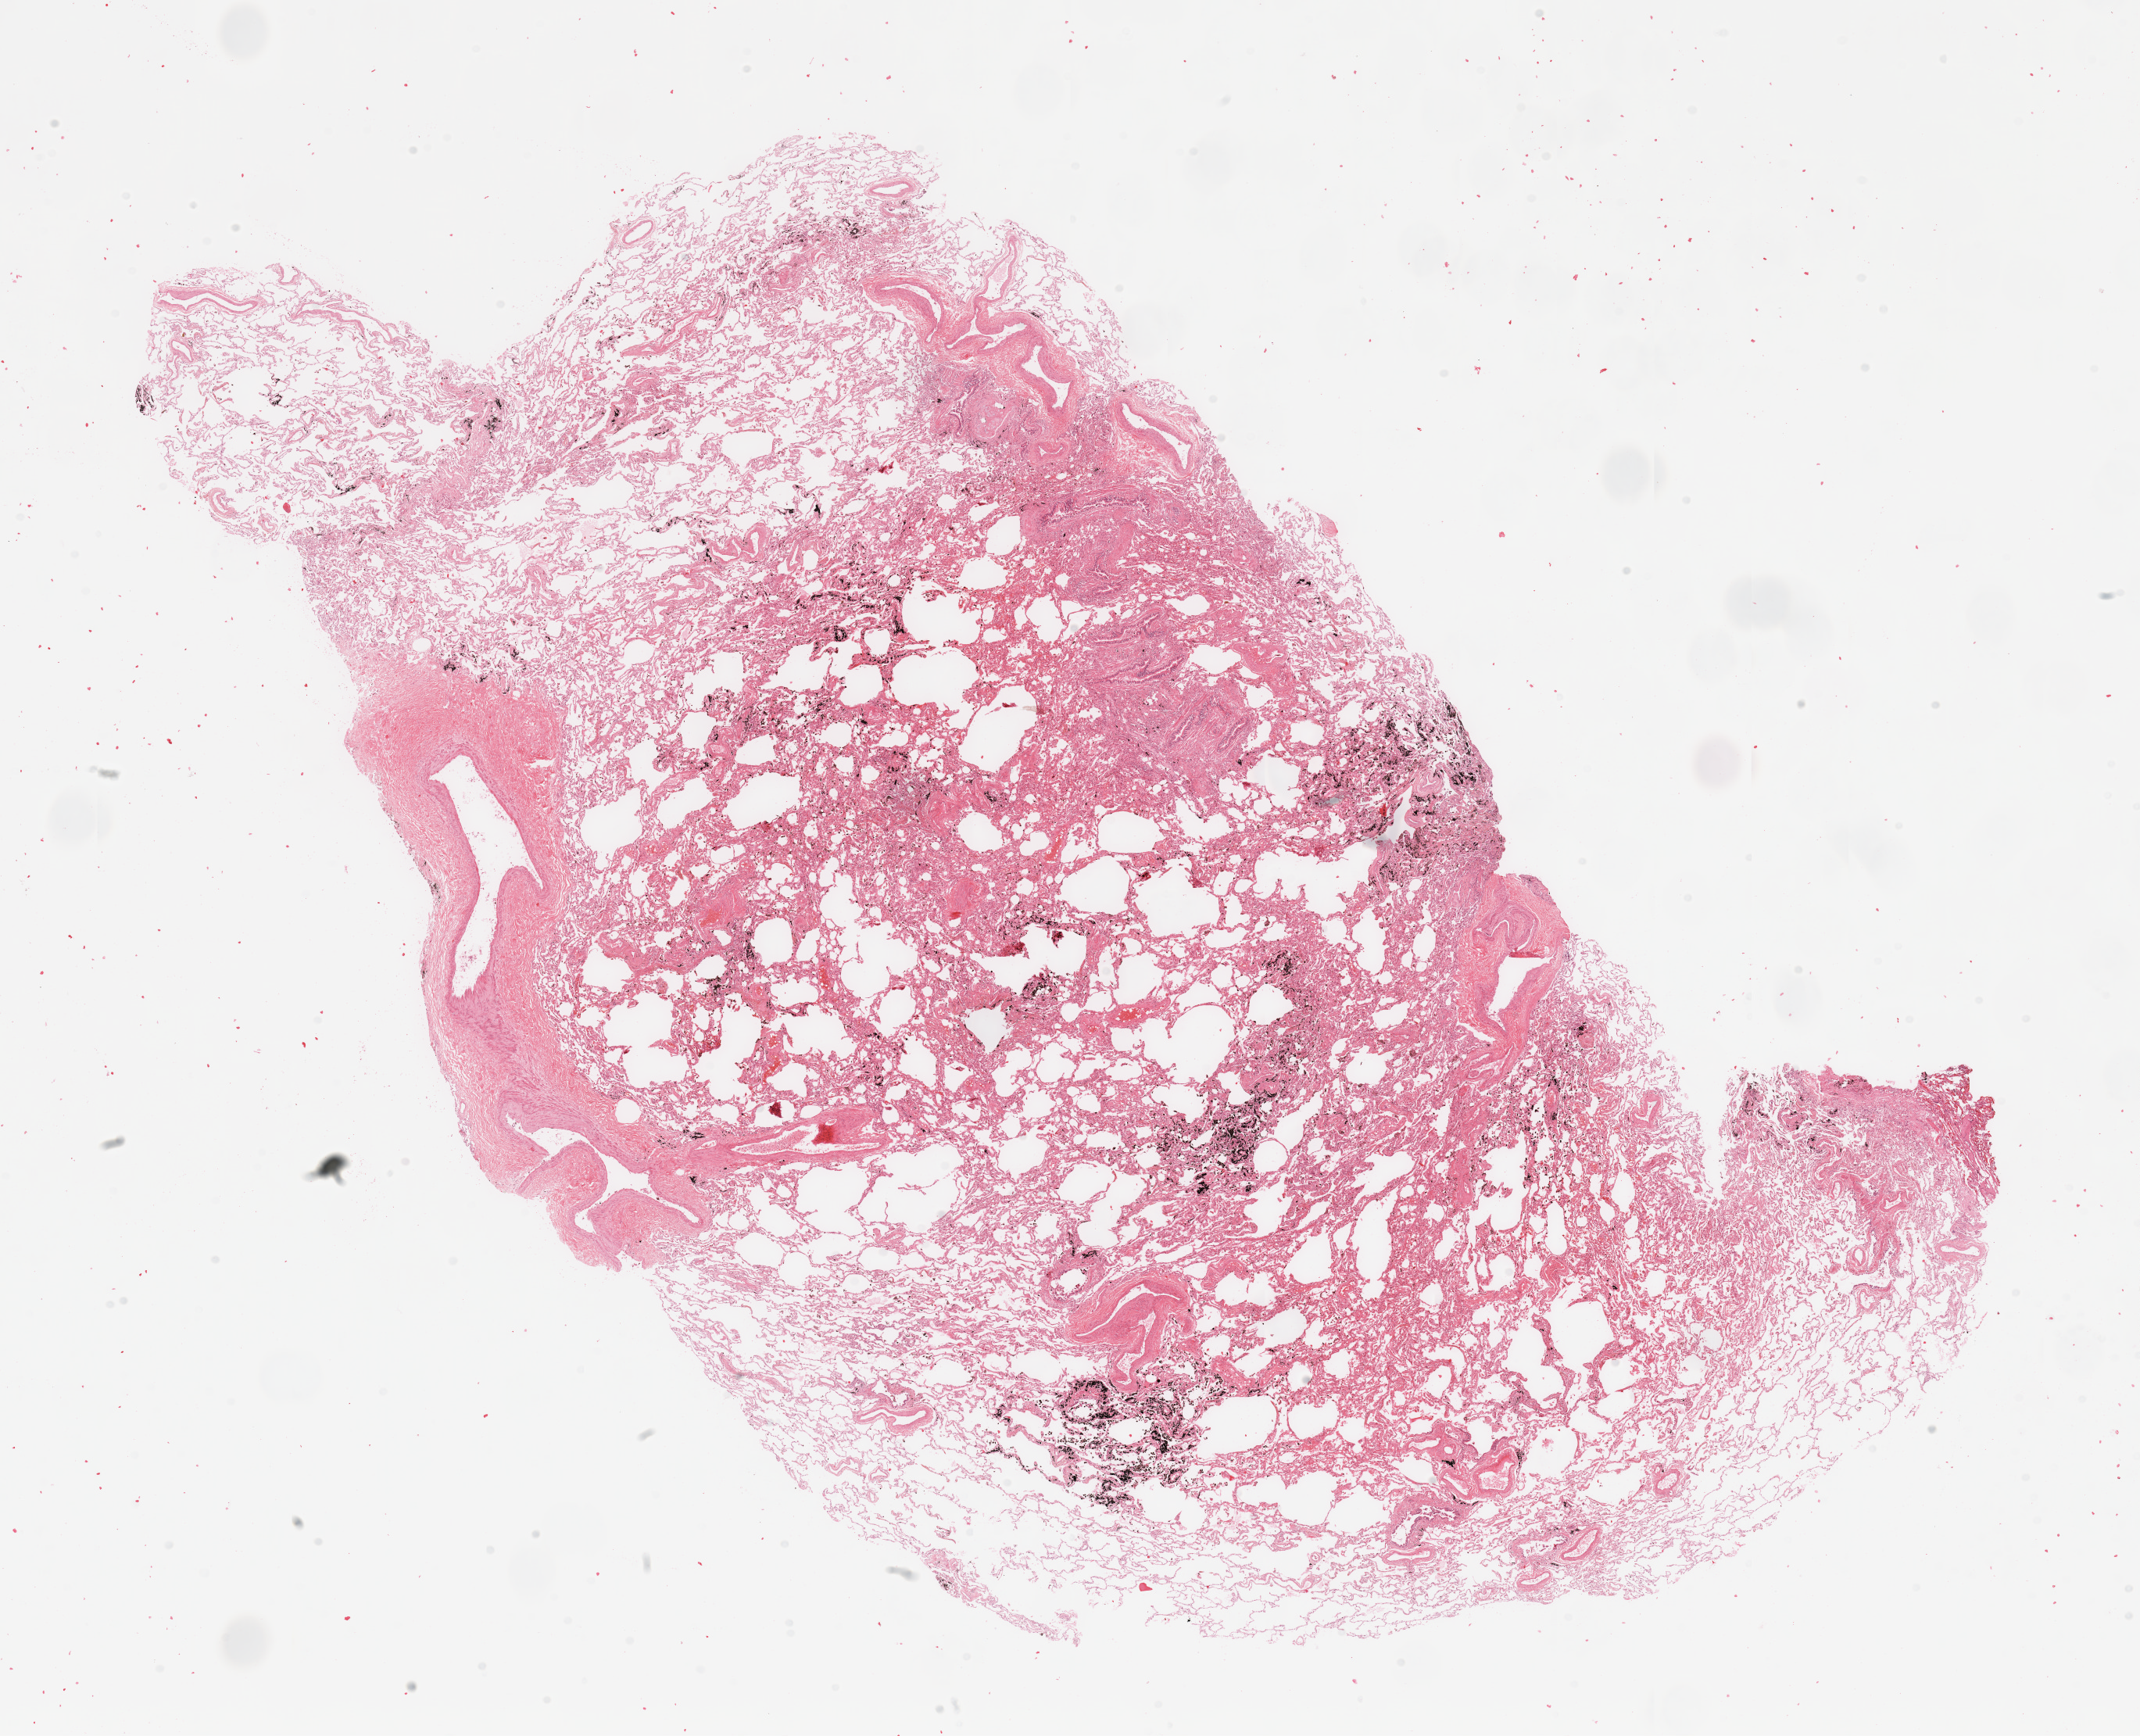
H&E-stained whole-slide image, a low-resolution overview of the entire scanned area, about 21.7 x 17.6 mm (from a 20x scan); lung, normal (non-tumour) tissue. Male, 72 y/o.
* this section: normal (non-tumour) tissue from the same patient
* patient diagnosis: Adenocarcinoma, NOS